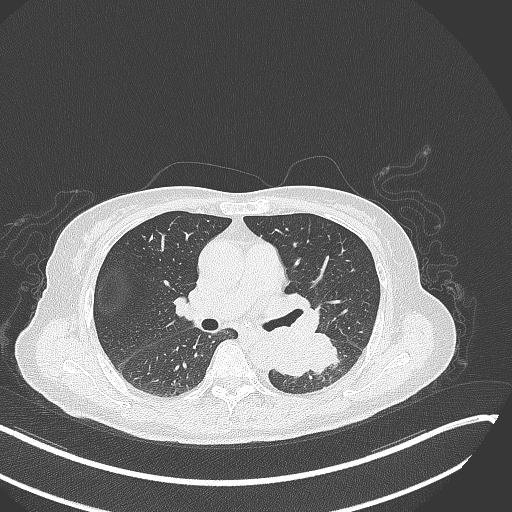
Chest CT, one axial slice; slice 160 of 342 in the series (ordered by position); lung window (W 1500 / L -600 HU); 512 × 512 image matrix, field of view 400 × 400 mm. Patient: female, 64 years. Case-level facts recorded for this patient, not image findings: clinical TNM (as recorded): T3 N1 M1; histopathological grade: G3.
Annotated regions visible in this slice (rectangle marked by the reading radiologist):
- lung tumour (recorded histology: small cell carcinoma): bounding box [x1, y1, x2, y2] px = [270, 333, 344, 379]